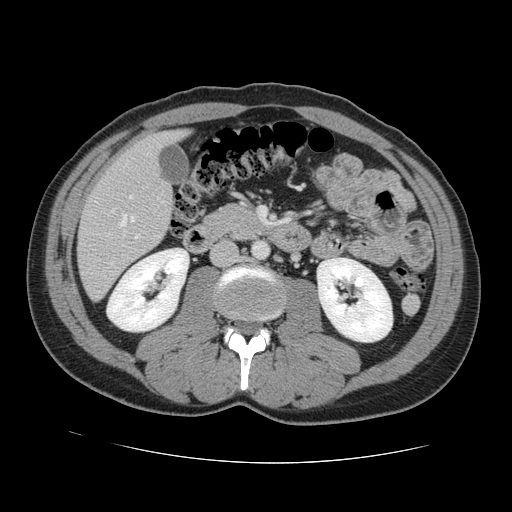
Contrast-enhanced abdominal CT, one axial slice. Position 45 of 131 along the scan axis. 120 kVp. Intravenous contrast given. Soft-tissue window (W 400 / L 40 HU). 2.5 mm slice thickness. 512 × 512 image matrix, field of view 380 × 380 mm. Male patient, age 40 years. From the clinical record (not read from this slice): diagnosis: colorectal cancer liver metastases, imaged before liver resection; multiple liver metastases: yes; largest metastasis: 2.9 cm; disease in both lobes: yes.
Structures marked on this image (expert manual segmentation):
- hepatic veins: bounding box [x1, y1, x2, y2] px = [120, 215, 135, 226]
- liver: [78, 132, 184, 299]
- planned liver remnant (the part of the liver to remain after resection): [128, 132, 184, 165]
- portal vein (with intrahepatic branches): [129, 195, 139, 239]